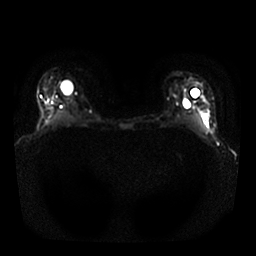
Breast MRI, one axial slice; position 19 of 25 along the scan axis; diffusion-weighted series; image 2 of 4 stored at this slice position (different b-values; order by instance number); 1.5 T; 4 mm slice thickness; 256 × 256 image matrix, field of view 340 × 340 mm. Female patient.
Annotated regions visible in this slice (expert manual segmentation):
- tumour on diffusion-weighted imaging: bounding box [x1, y1, x2, y2] px = [200, 96, 210, 117]